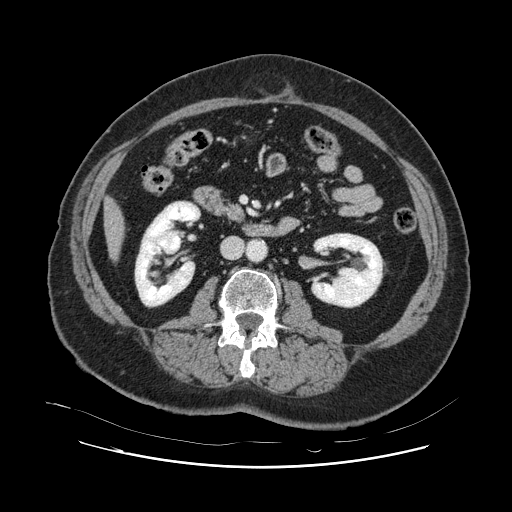
Contrast-enhanced abdominal CT, one axial slice; position 22 of 132 along the scan axis; 120 kVp; intravenous contrast given; soft-tissue window (W 400 / L 40 HU); 512 × 512 image matrix, field of view 391 × 391 mm. Female patient, age 73 years. Case-level facts recorded for this patient, not image findings: diagnosis: colorectal cancer liver metastases, imaged before liver resection; multiple liver metastases: no; largest metastasis: 7 cm; disease in both lobes: no.
Annotated regions visible in this slice (expert manual segmentation):
- liver: bounding box [x1, y1, x2, y2] px = [106, 202, 123, 256]
- planned liver remnant (the part of the liver to remain after resection): [106, 202, 123, 256]